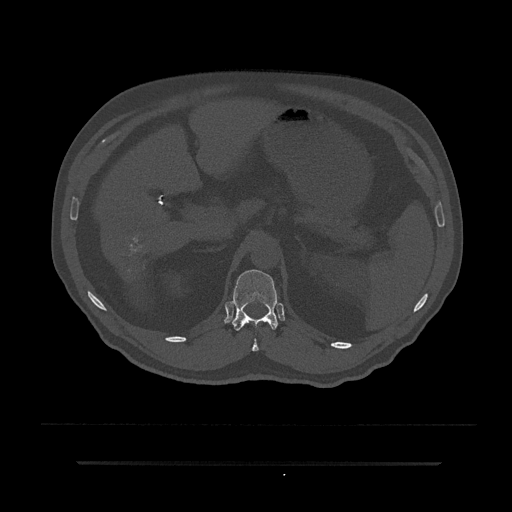
CT including the spine, one axial slice; 120 kVp; bone window (W 1800 / L 400 HU); 0.5 mm slice thickness; 512 × 512 image matrix, field of view 464 × 464 mm. Male patient, age 59 years. Case-level facts recorded for this patient, not image findings: primary cancer: bile ducts; vertebrae with lytic lesions (as recorded): T10.
Outlined on this slice (semi-automatically segmented with operator editing):
- T12 vertebra: bounding box <232,269,279,352> (left, top, right, bottom; pixels)